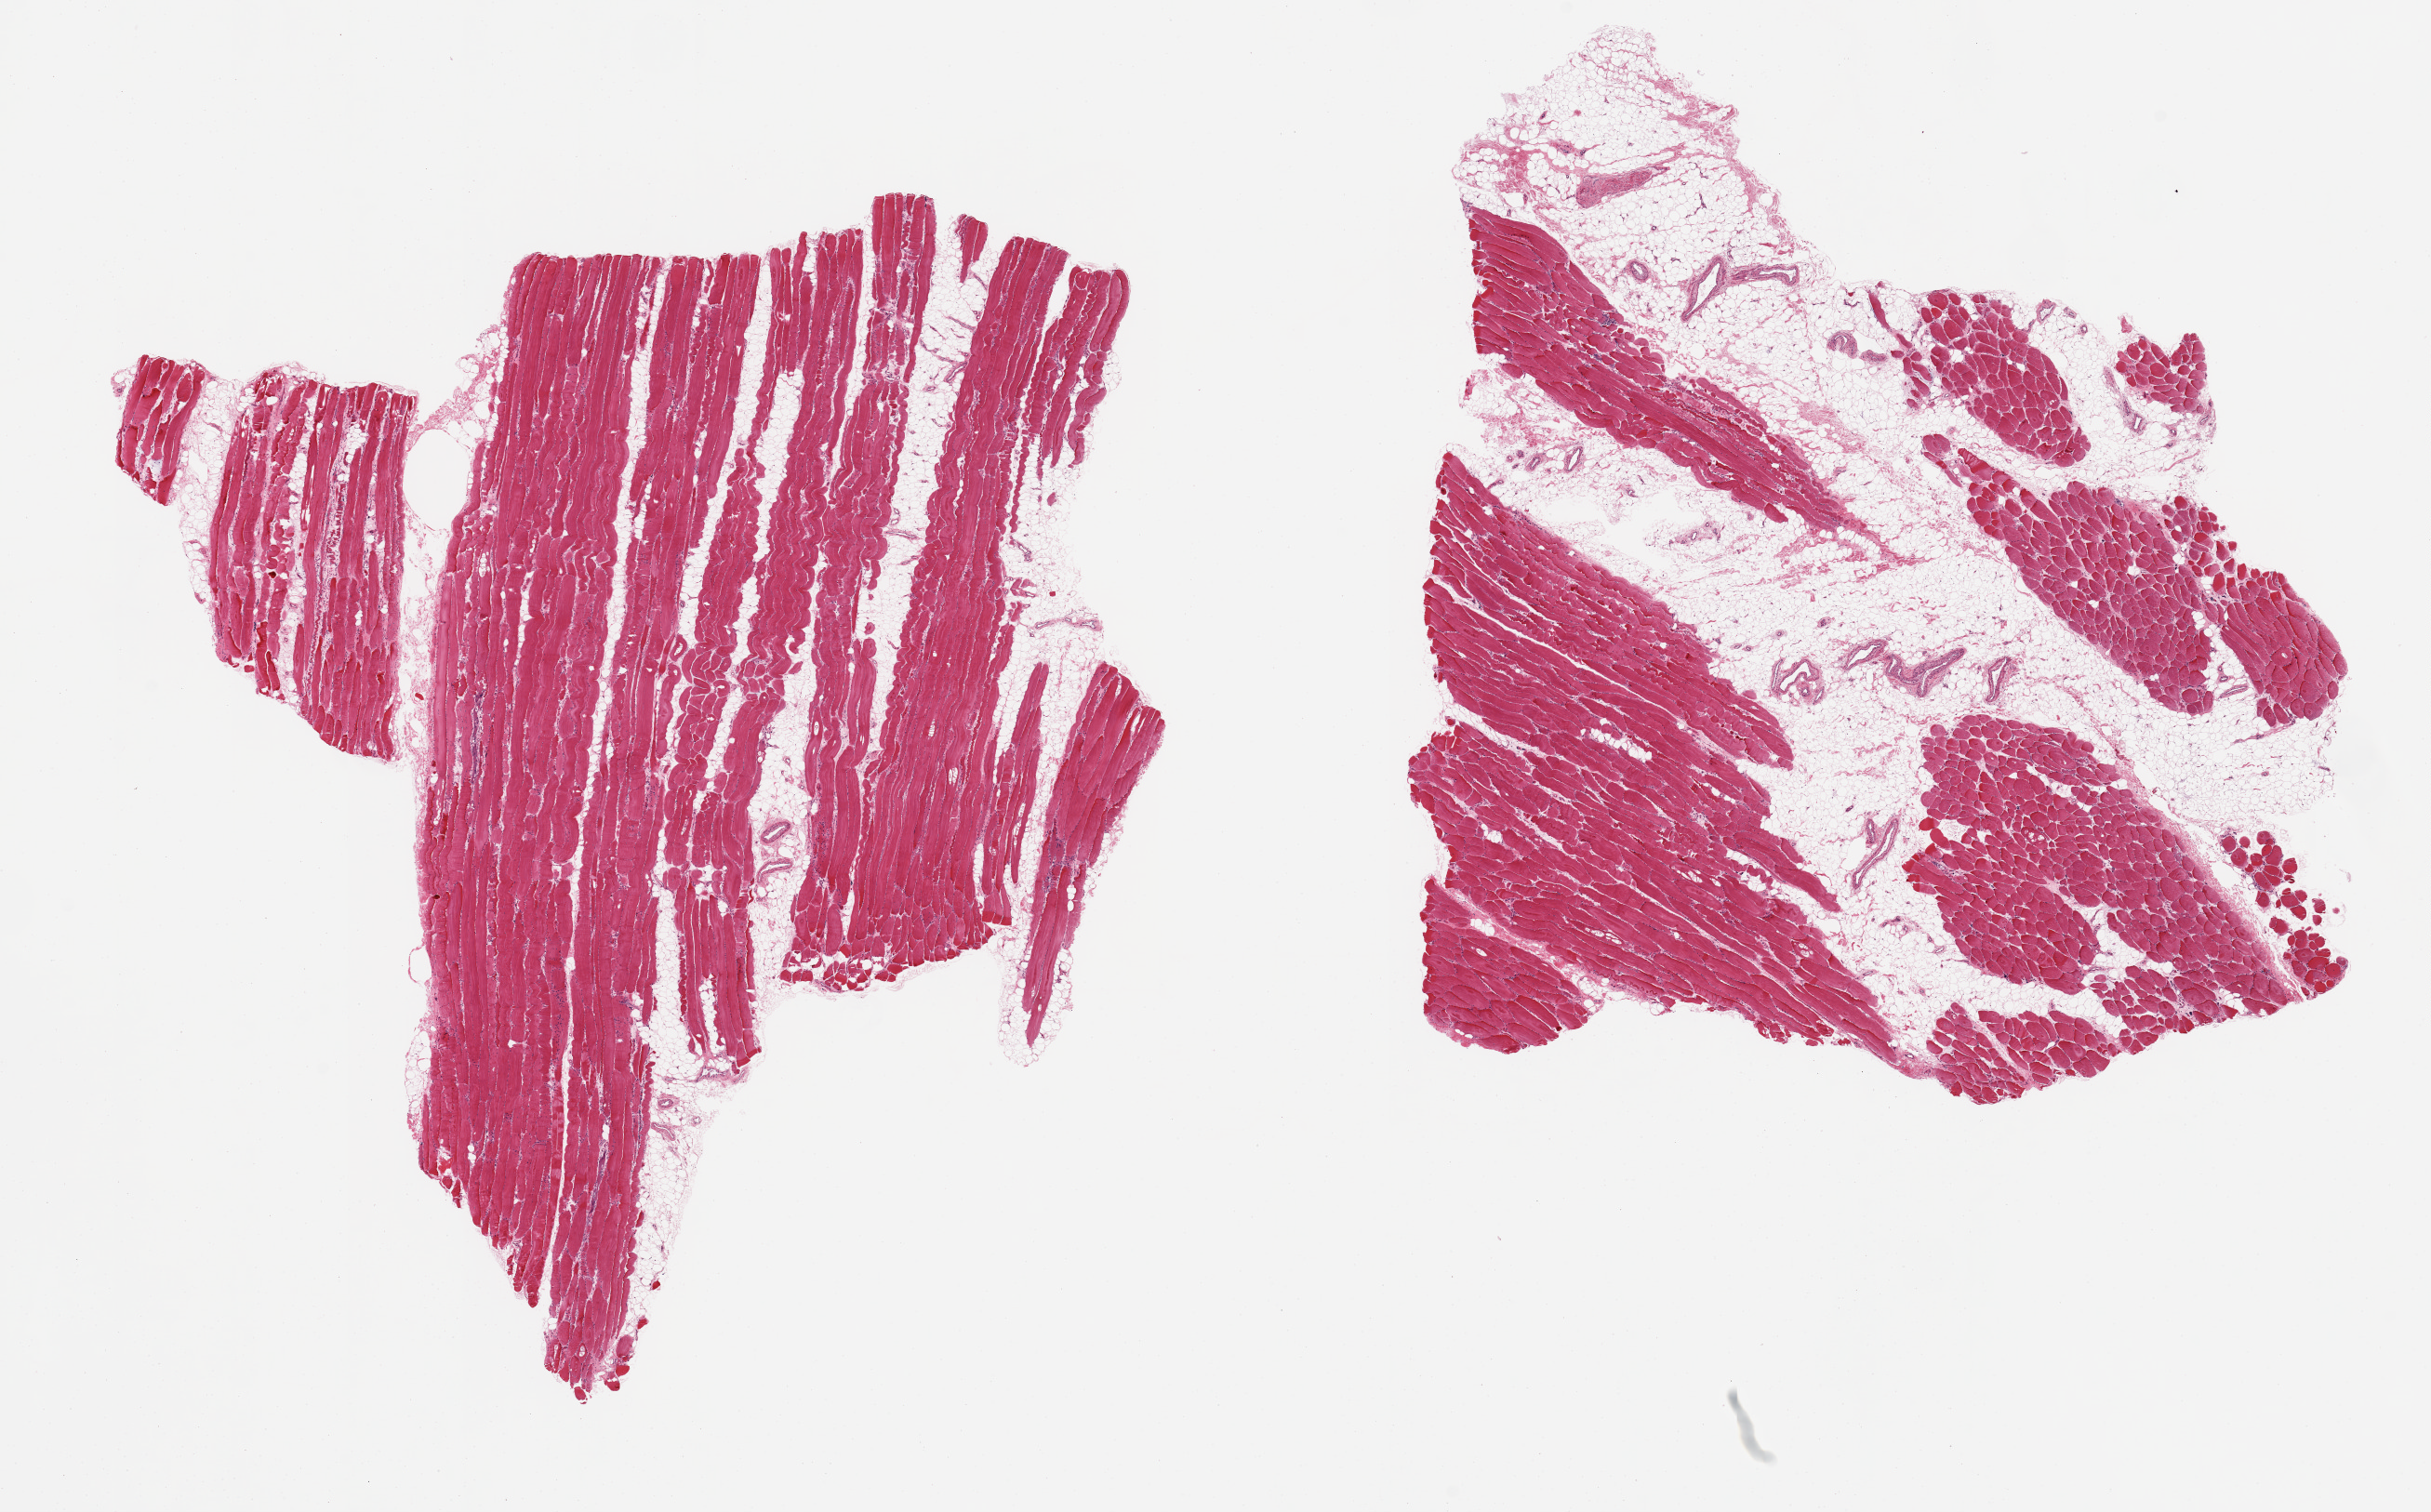
Digitized hematoxylin and eosin (H&E)-stained section, whole scanned area (about 20.7 x 12.9 mm, acquisition: 20x scan) shown as a low-resolution overview. PAXgene-fixed paraffin-embedded (PFPE) section. Target tissue: skeletal muscle. Tissue donor sample. Donor: male.
Pathologist's review note for this sample: 2 pieces. Moderate atrophy. 40 and 10% internal fat.